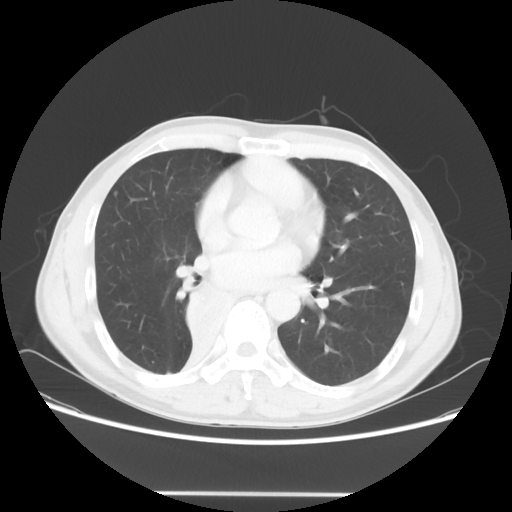
Chest CT, one axial slice; slice 30 of 62 in the series (ordered by position); 120 kVp; lung window (W 1500 / L -600 HU); 5 mm slice thickness; 512 × 512 image matrix, field of view 393 × 393 mm. Patient: male, 47 years. From the clinical record (not read from this slice): clinical TNM (as recorded): T2 N0 M0; histopathological grade: G2.
Outlined on this slice (bounding box drawn by a radiologist):
- lung tumour (recorded histology: squamous cell carcinoma): bounding box <184,283,245,356> (left, top, right, bottom; pixels)